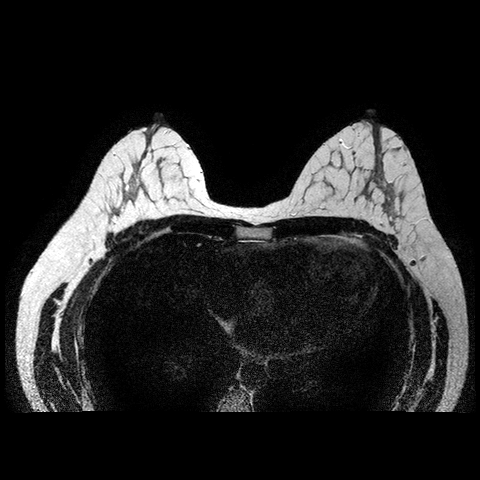
Breast MRI examination; 2 images, each one mid-volume slice chosen by position. Patient in her 40s.
Image 1: fluid-sensitive (T2/STIR) axial slice, slice 43 of 84, 2 mm slice thickness.
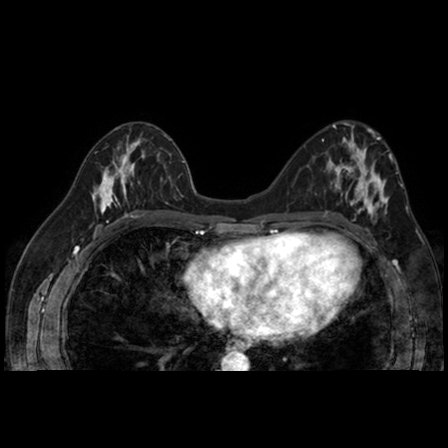
Image 2: axial dynamic contrast-enhanced T1-weighted image, series "AX BLISS_AUTO SENSE", slice 43 of 84, dynamic phase 5 of 8.
Patient-level pathology facts (from the clinical record, not from the images): pathology diagnosis: ductal CA in situ (left breast); pathology report notes: Ductal carcinoma in-situ.